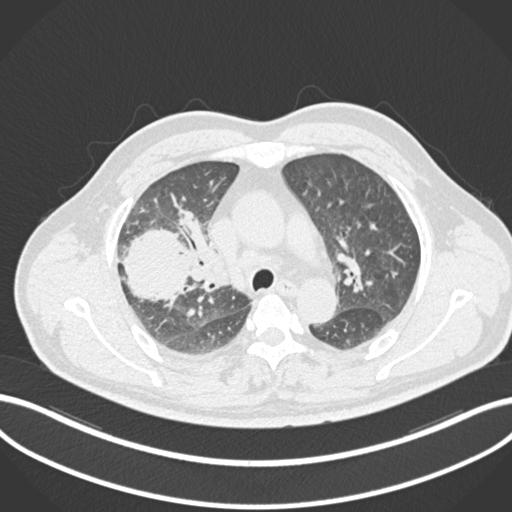
Chest CT, one axial slice. Position 657 of 852 along the scan axis. Reconstruction kernel B30f. Lung window (W 1500 / L -600 HU). 1 mm slice thickness. 512 × 512 image matrix, field of view 400 × 400 mm. Patient: male, 55 years. Case-level facts recorded for this patient, not image findings: clinical TNM (as recorded): T3 N2 M1.
Outlined on this slice (rectangle marked by the reading radiologist):
- lung tumour (recorded histology: adenocarcinoma): bounding box (x1, y1, x2, y2) in pixels: (116, 228, 196, 306)